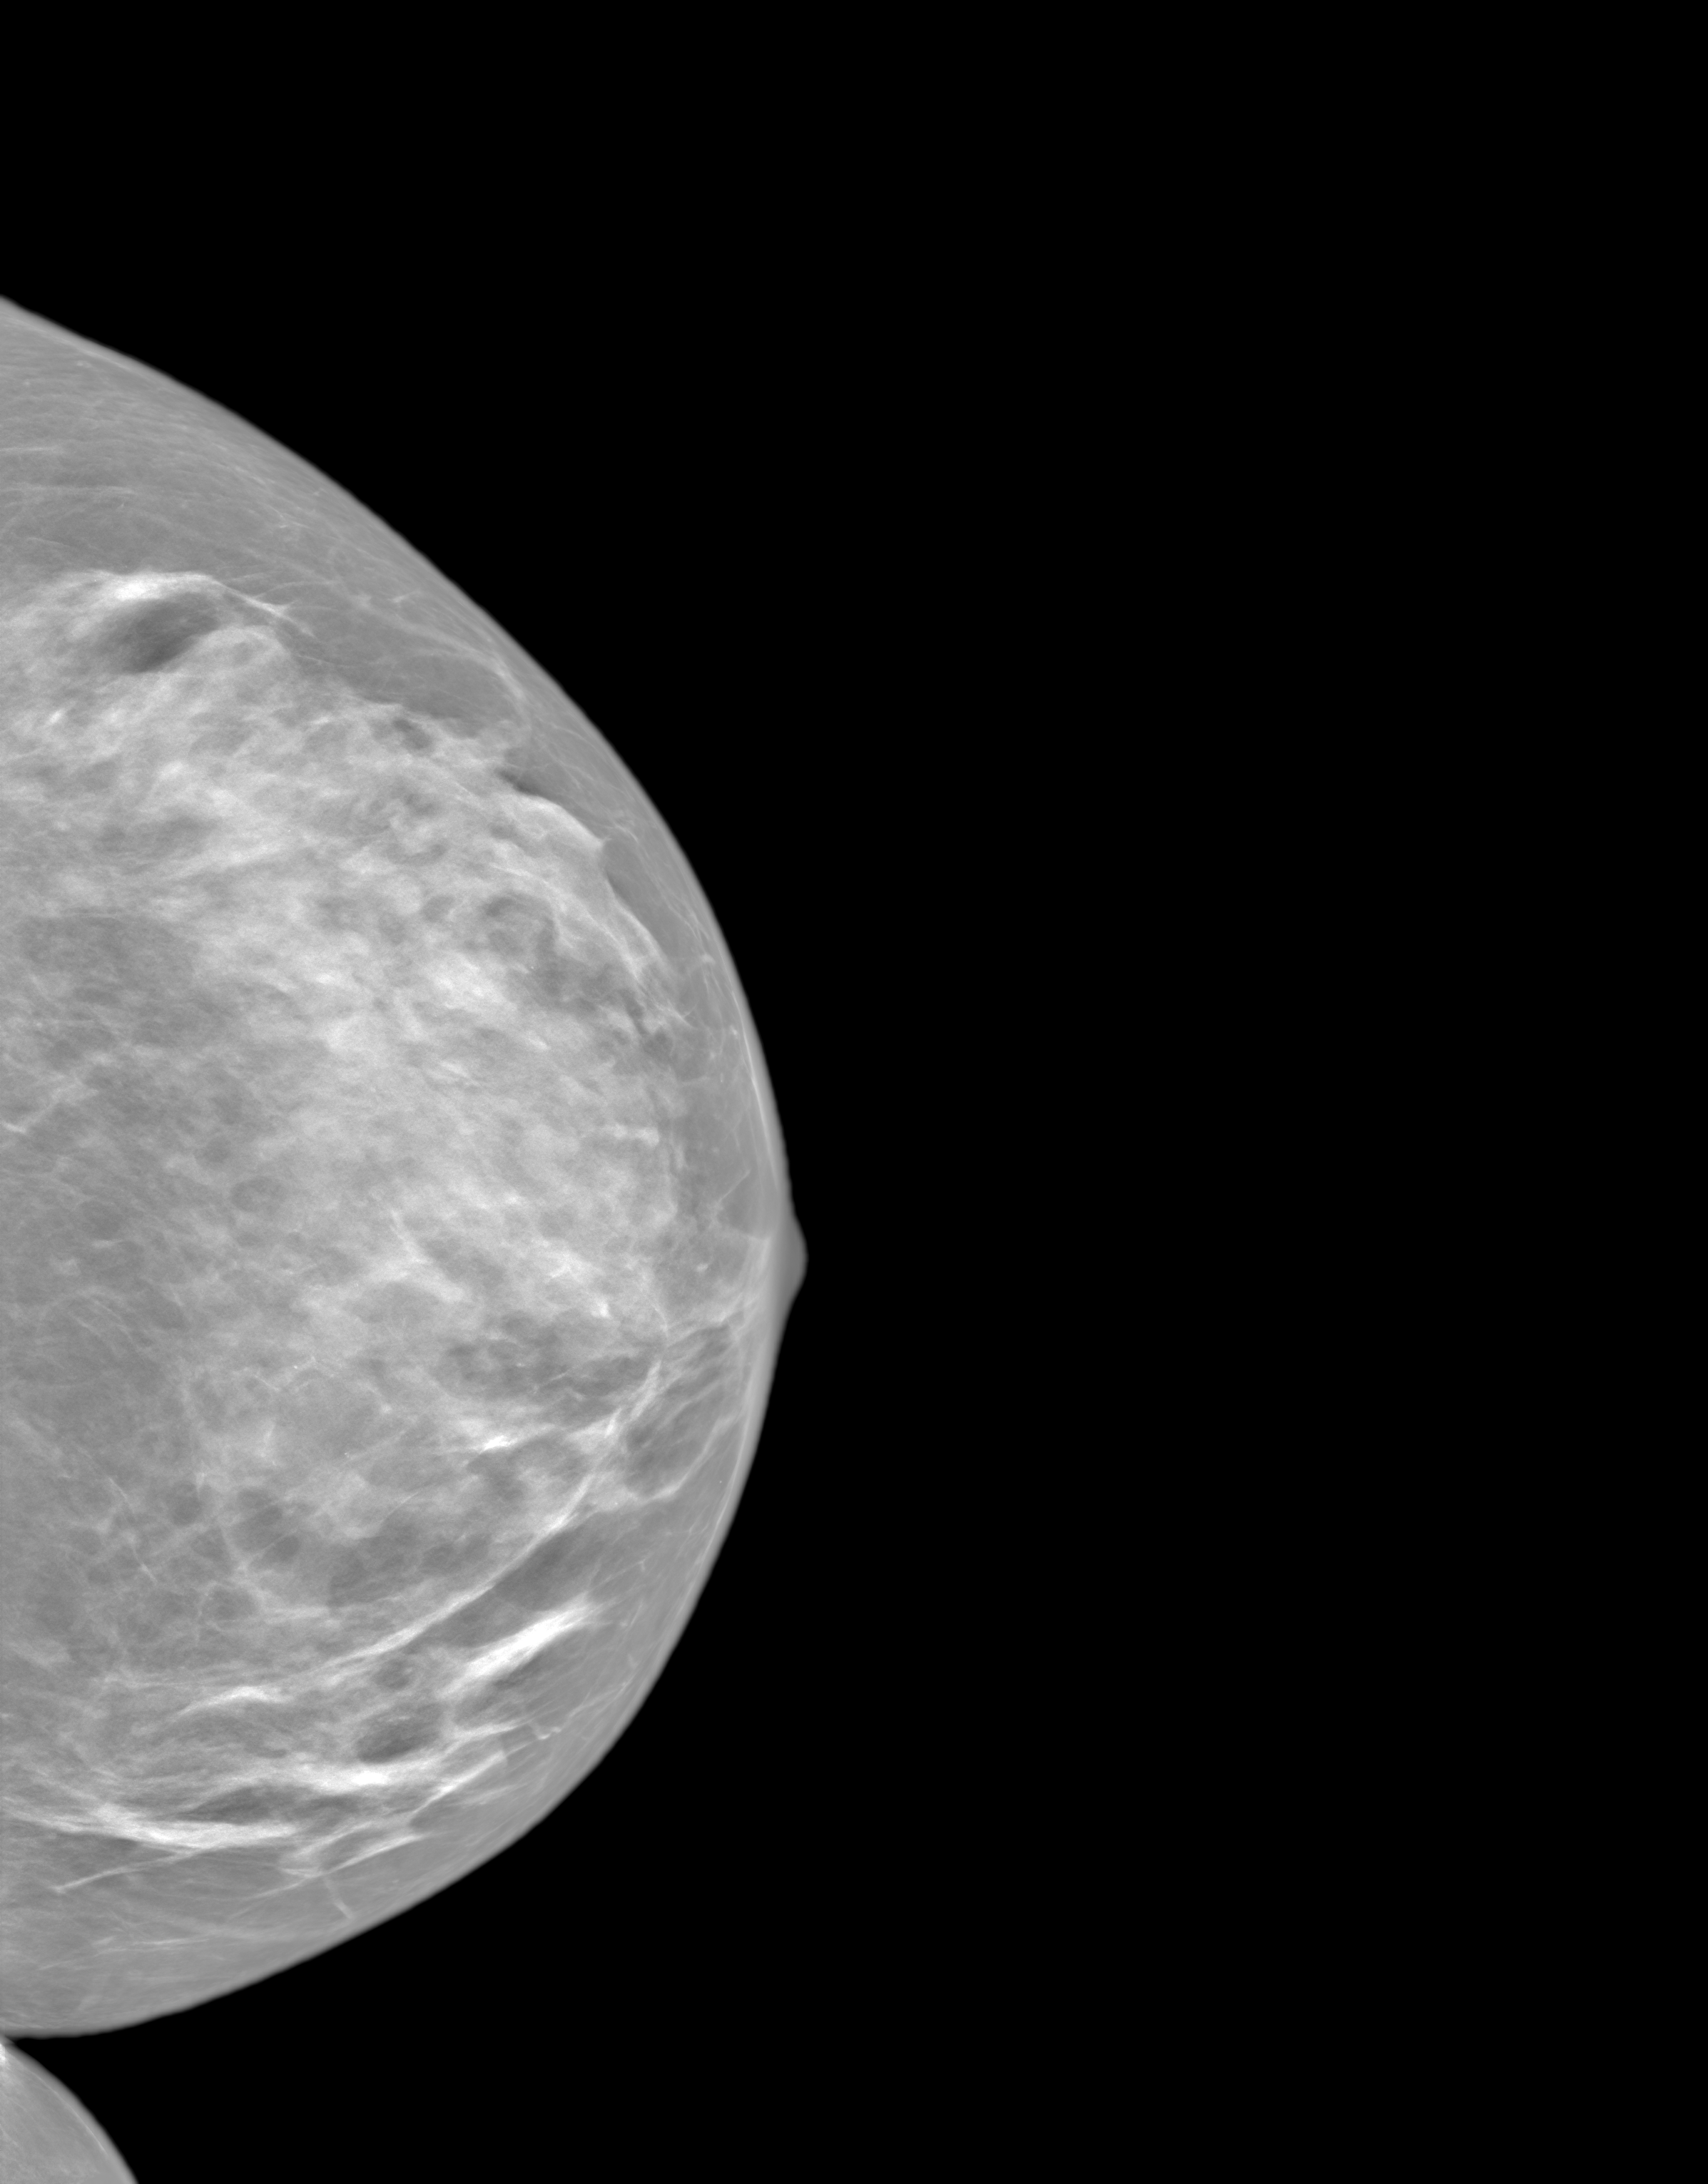
Annual screening mammography examination, system: SenoIris_1SP1.1(421). Patient: female, 64 years.
Image type: synthesized 2-D view from tomosynthesis. Breast: left. Projection: CC view. BI-RADS breast density category at the screening exam (both breasts, scale 1–4): 4. Final BI-RADS category for the screening round (tomosynthesis exam, both breasts): category 2. Recall: no recall after this screen.